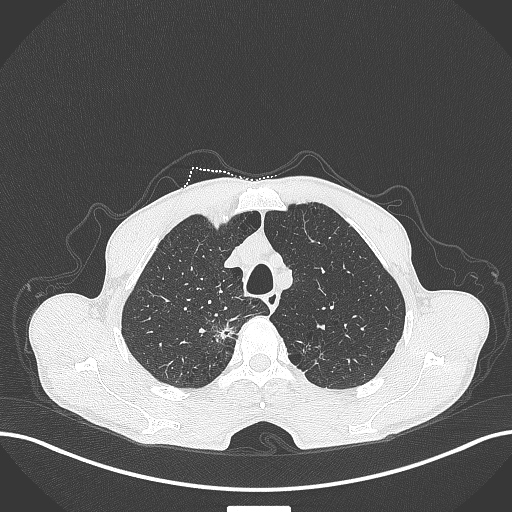
Chest CT, one axial slice. 120 kVp. Lung window (W 1500 / L -600 HU). 512 × 512 image matrix, field of view 400 × 400 mm. Patient: male, 70 years. From the clinical record (not read from this slice): clinical TNM (as recorded): T1a N0 M0; histopathological grade: G1-2.
Structures marked on this image (bounding box drawn by a radiologist):
- lung tumour (recorded histology: adenocarcinoma): bounding box (x1, y1, x2, y2) in pixels: (218, 321, 236, 346)